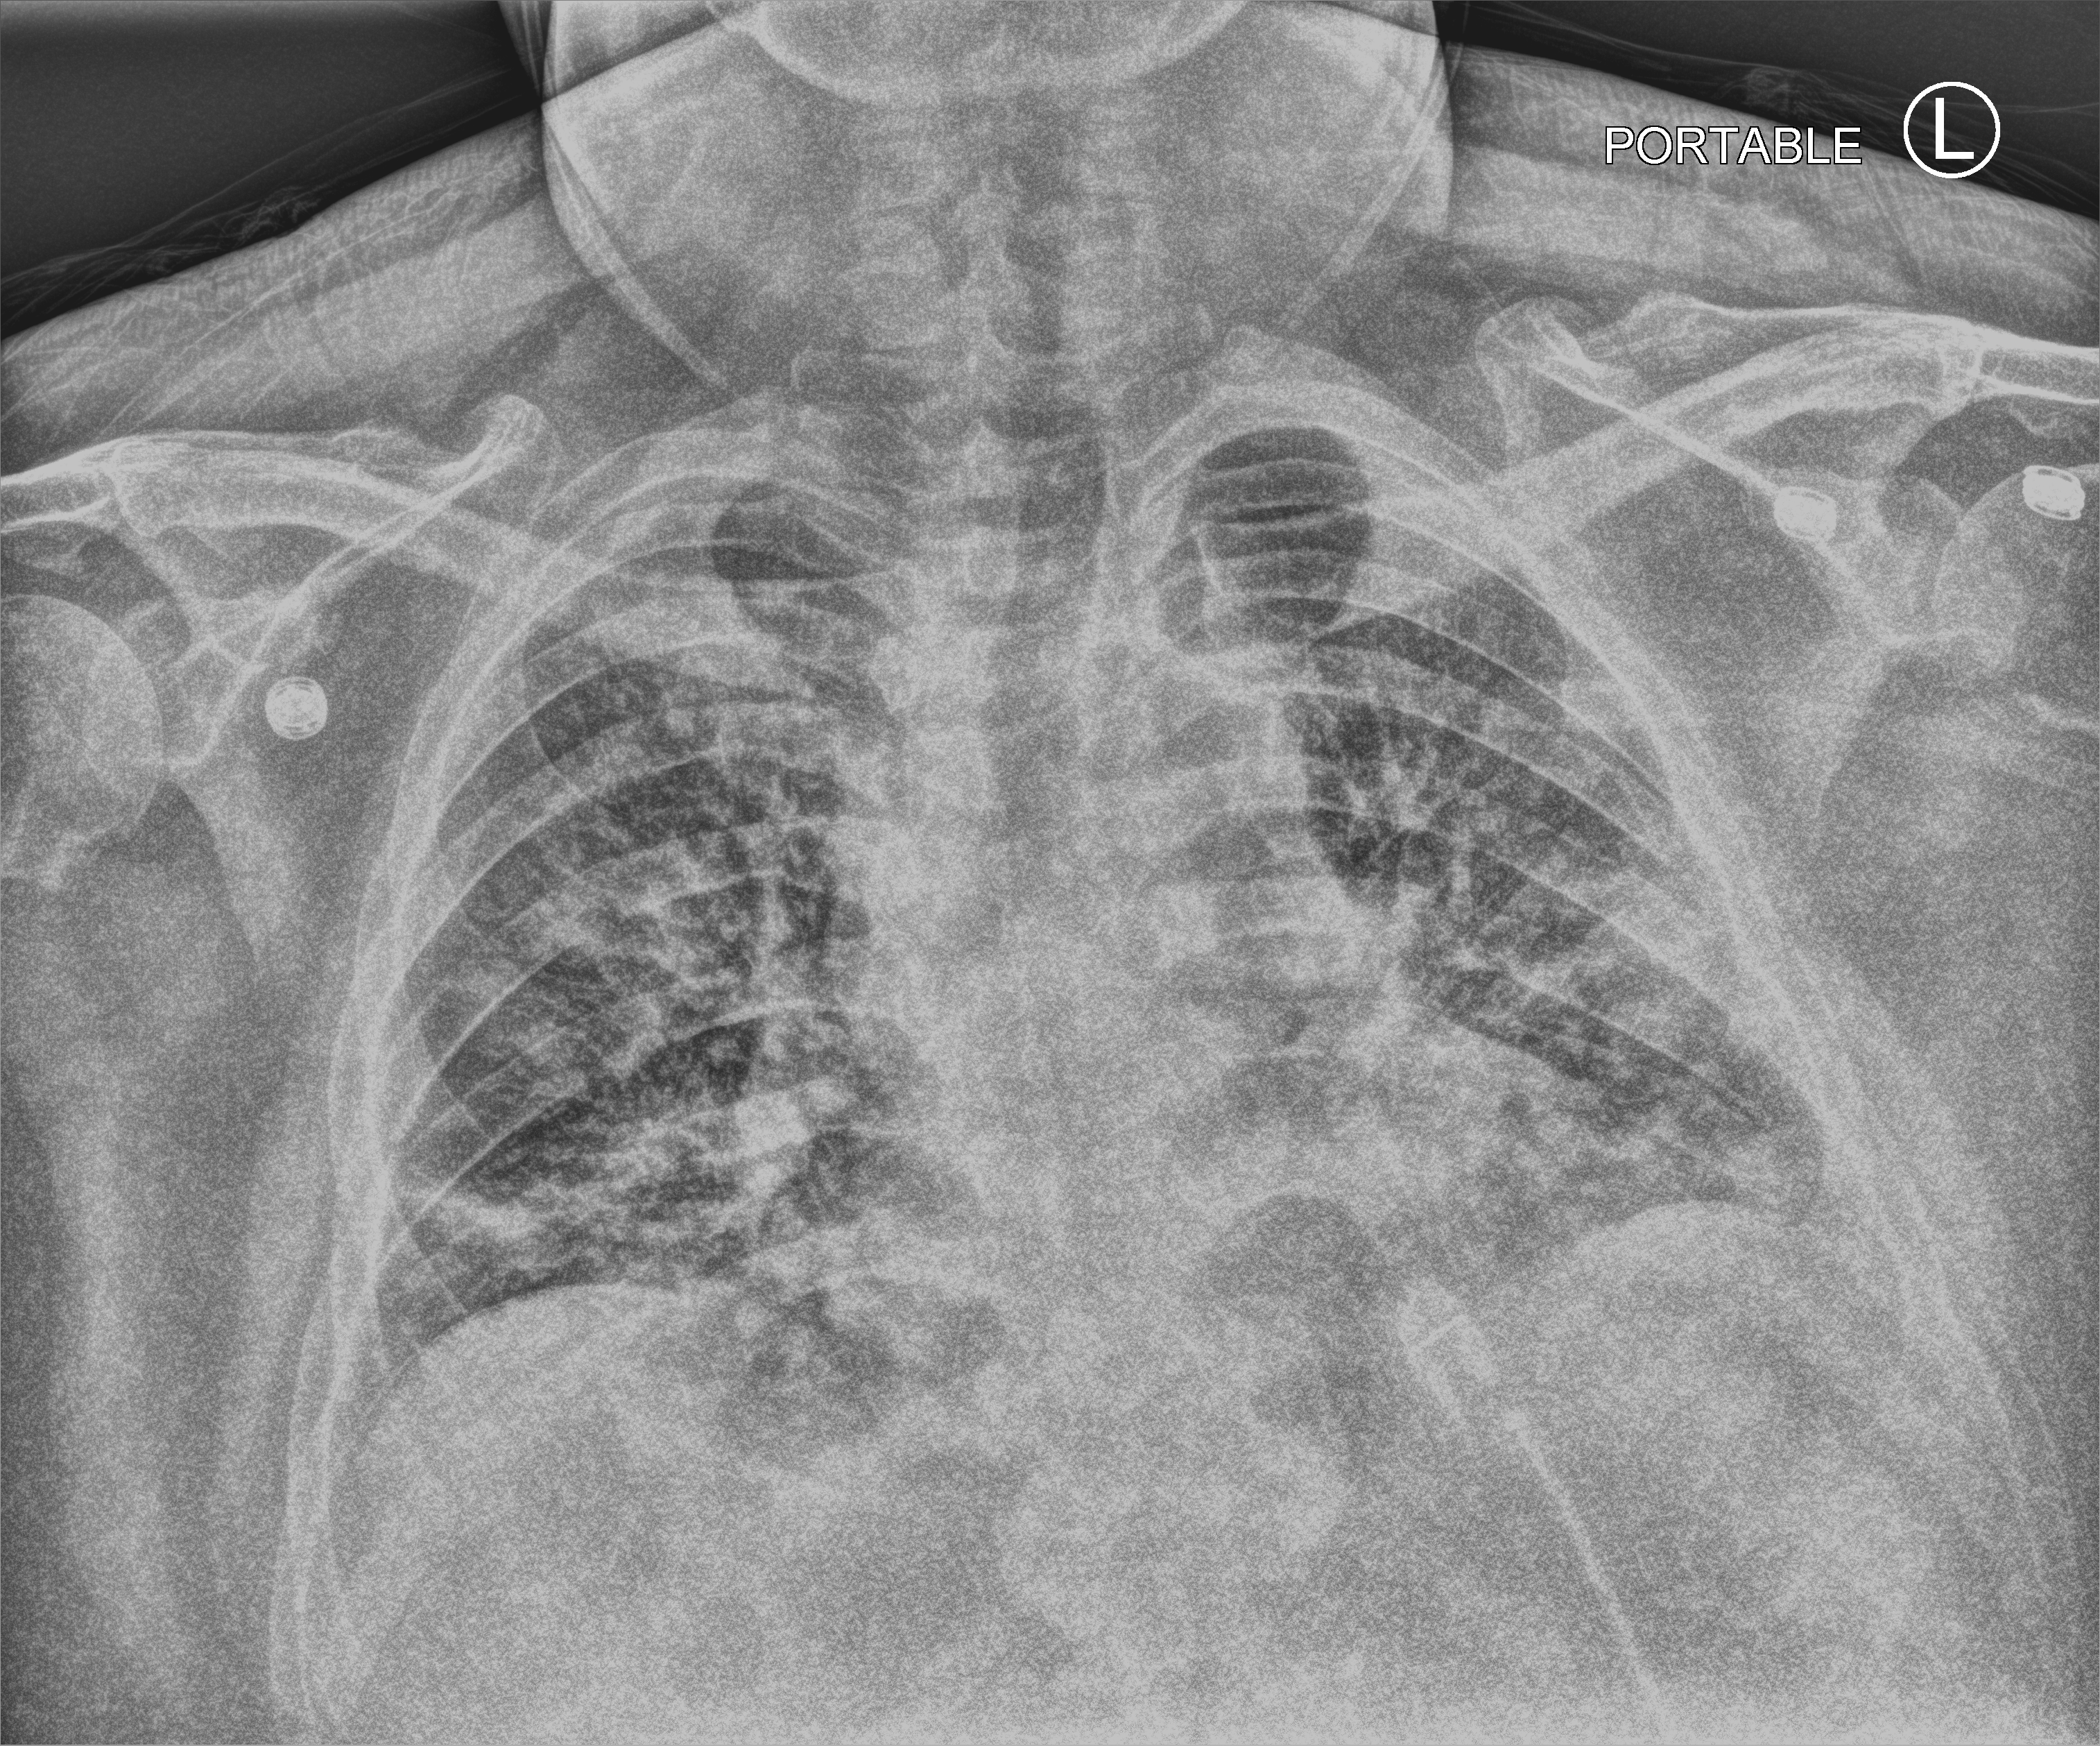
Bedside chest radiograph (computed radiography). Male patient hospitalised with COVID-19, age 18–59 years.
Admission-level facts for this patient (not findings on this image; timing relative to this image not recorded): length of hospital stay: 25 days; COPD (admission record): no.